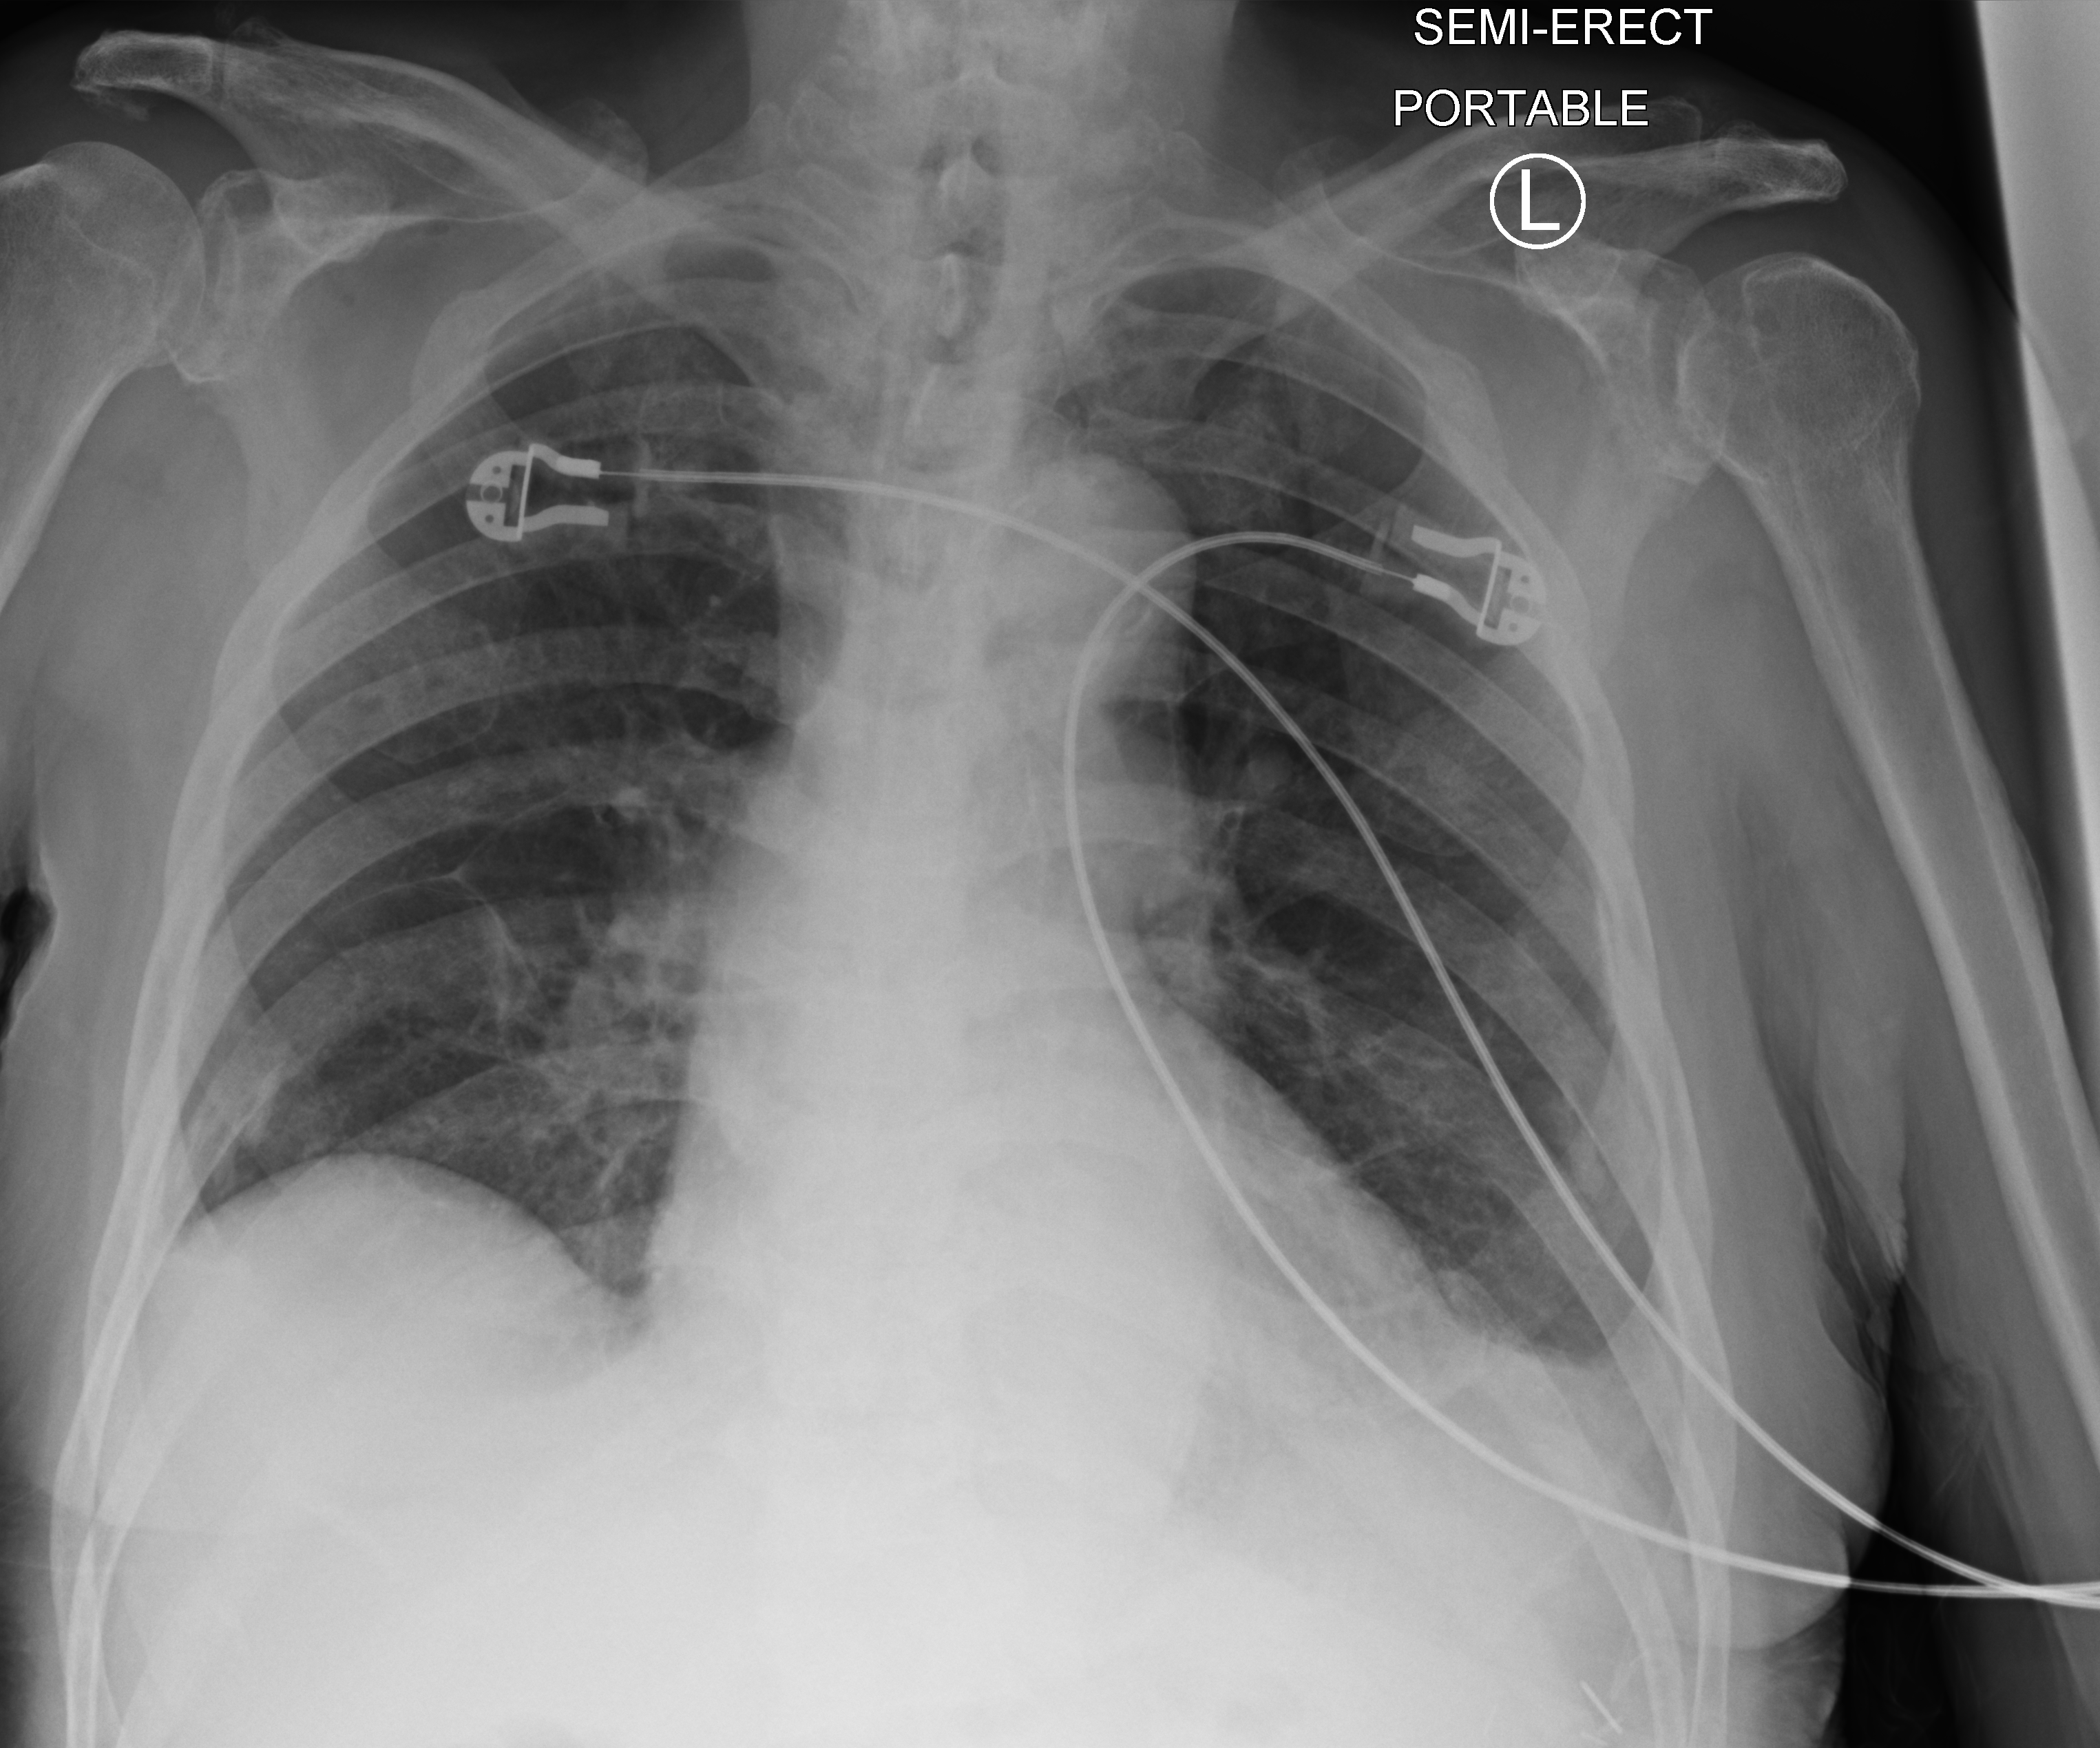
Portable chest radiograph. Male patient hospitalised with COVID-19, age 75–90 years.
Admission-level facts for this patient (not findings on this image; timing relative to this image not recorded): mechanically ventilated during this hospital stay: no; admitted to intensive care during this hospital stay: no; length of hospital stay: 12 days.